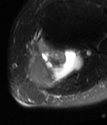
MRI of an extremity soft-tissue mass, one axial slice; T2-weighted fat-saturated; MR volume resampled by the dataset authors to the PET/CT grid (not the native acquisition matrix); 107 × 125 image matrix. Female patient. From the clinical record (not read from this slice): histological type: extraskeletal high grade osteogenic sarcoma; grade: high; site of the primary tumour: left calf.
Annotated regions visible in this slice (expert contour drawn on MRI and transferred to this co-registered scan by the dataset authors):
- gross tumour volume (mass): bounding box <26,45,84,89> (left, top, right, bottom; pixels)